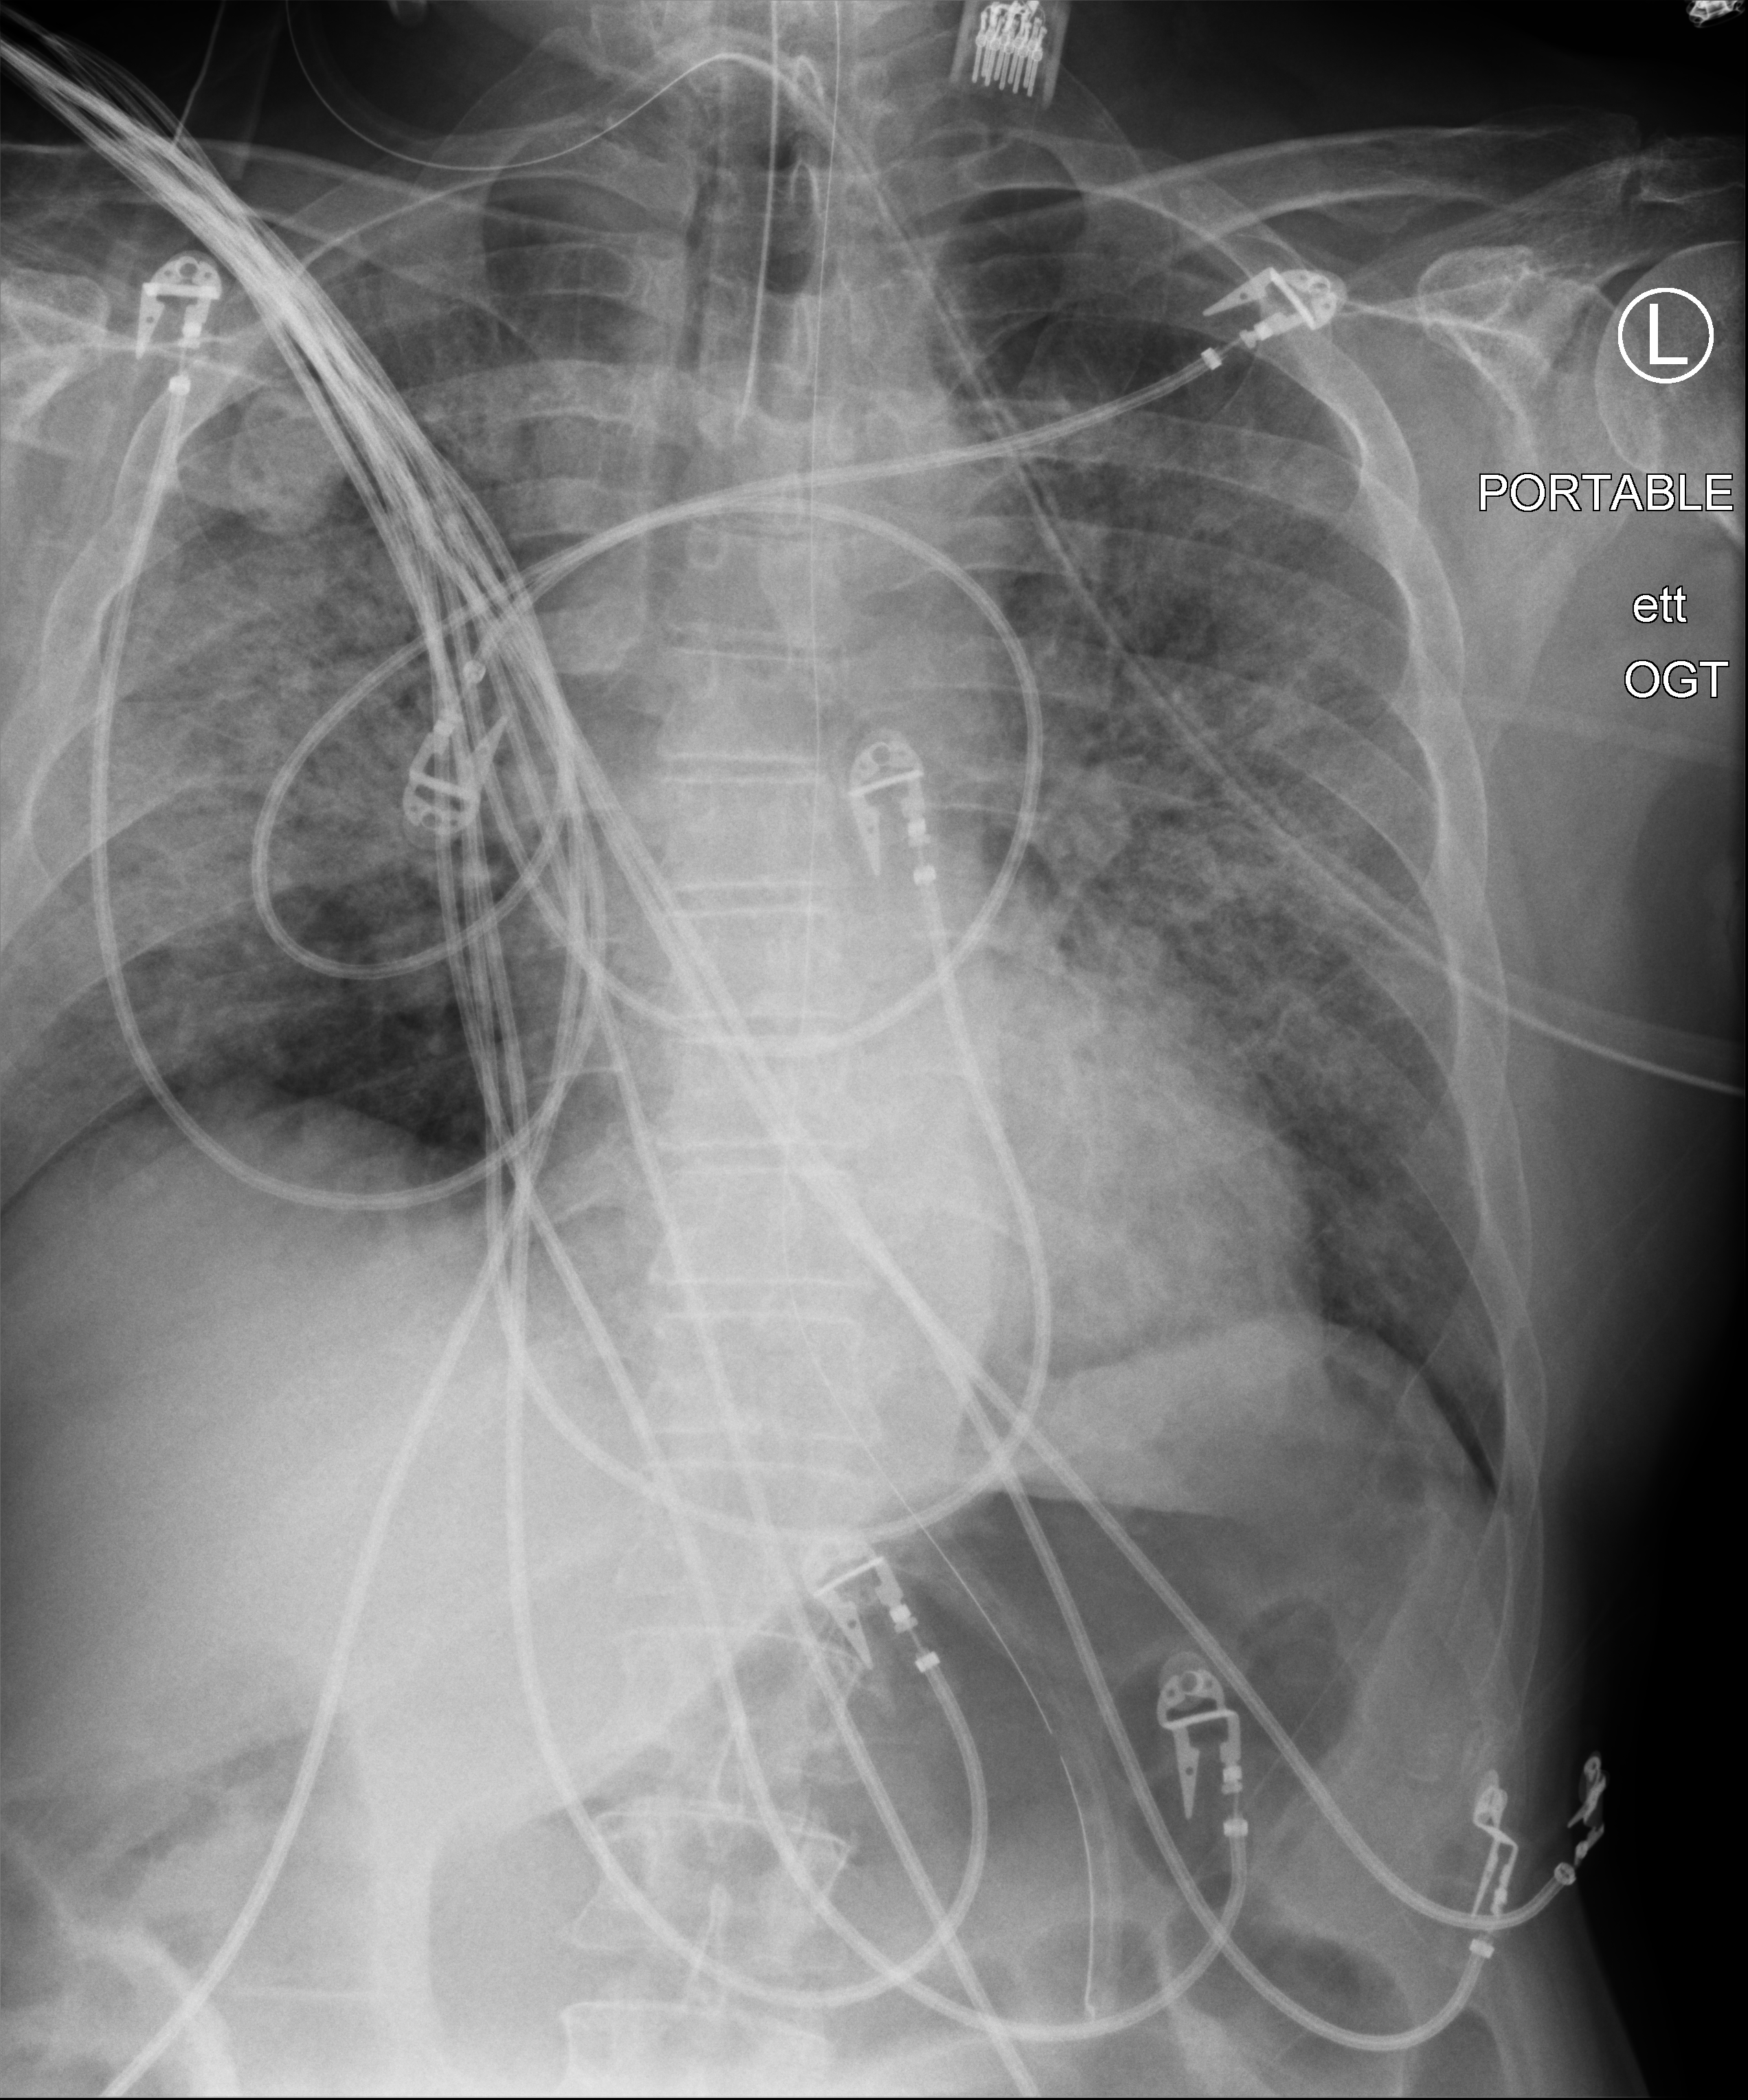
Chest X-ray (portable). Patient hospitalised with COVID-19; male, aged 60–74 years.
From the hospital-stay record, not from the radiograph (when in the stay this image was taken is not recorded): admitted to intensive care during this hospital stay: yes.